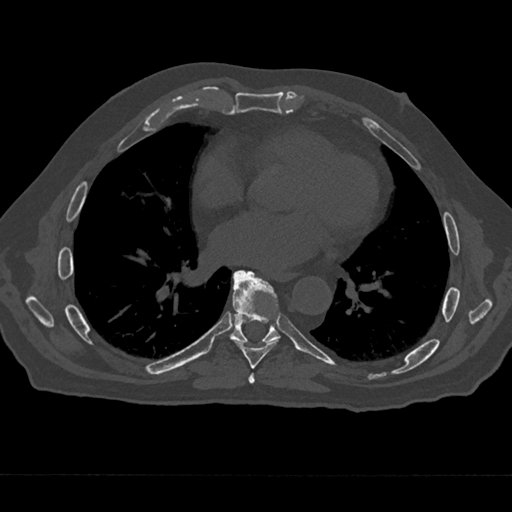
CT including the spine, one axial slice; slice 346 of 797 in the series (ordered by position); reconstruction kernel Br40s/3; 120 kVp; bone window (W 1800 / L 400 HU); 512 × 512 image matrix, field of view 377 × 377 mm. Male patient, age 75 years. Case-level facts recorded for this patient, not image findings: primary cancer: renal; vertebrae with lytic lesions (as recorded): T4.
Annotated regions visible in this slice (semi-automatic segmentation, software-assisted and operator-edited):
- T6 vertebra: bounding box [x1, y1, x2, y2] px = [248, 373, 255, 384]
- T7 vertebra: [234, 270, 280, 369]
- T8 vertebra: [230, 271, 280, 343]